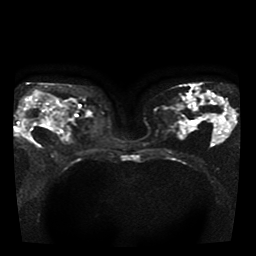
Breast MRI, one axial slice; slice 22 of 41 in the series (ordered by position); diffusion-weighted series; image 2 of 4 stored at this slice position (different b-values; order by instance number); 1.5 T; 256 × 256 image matrix, field of view 330 × 330 mm. Female patient.
Outlined on this slice (expert manual segmentation):
- tumour on diffusion-weighted imaging: bounding box (x1, y1, x2, y2) in pixels: (22, 120, 38, 143)